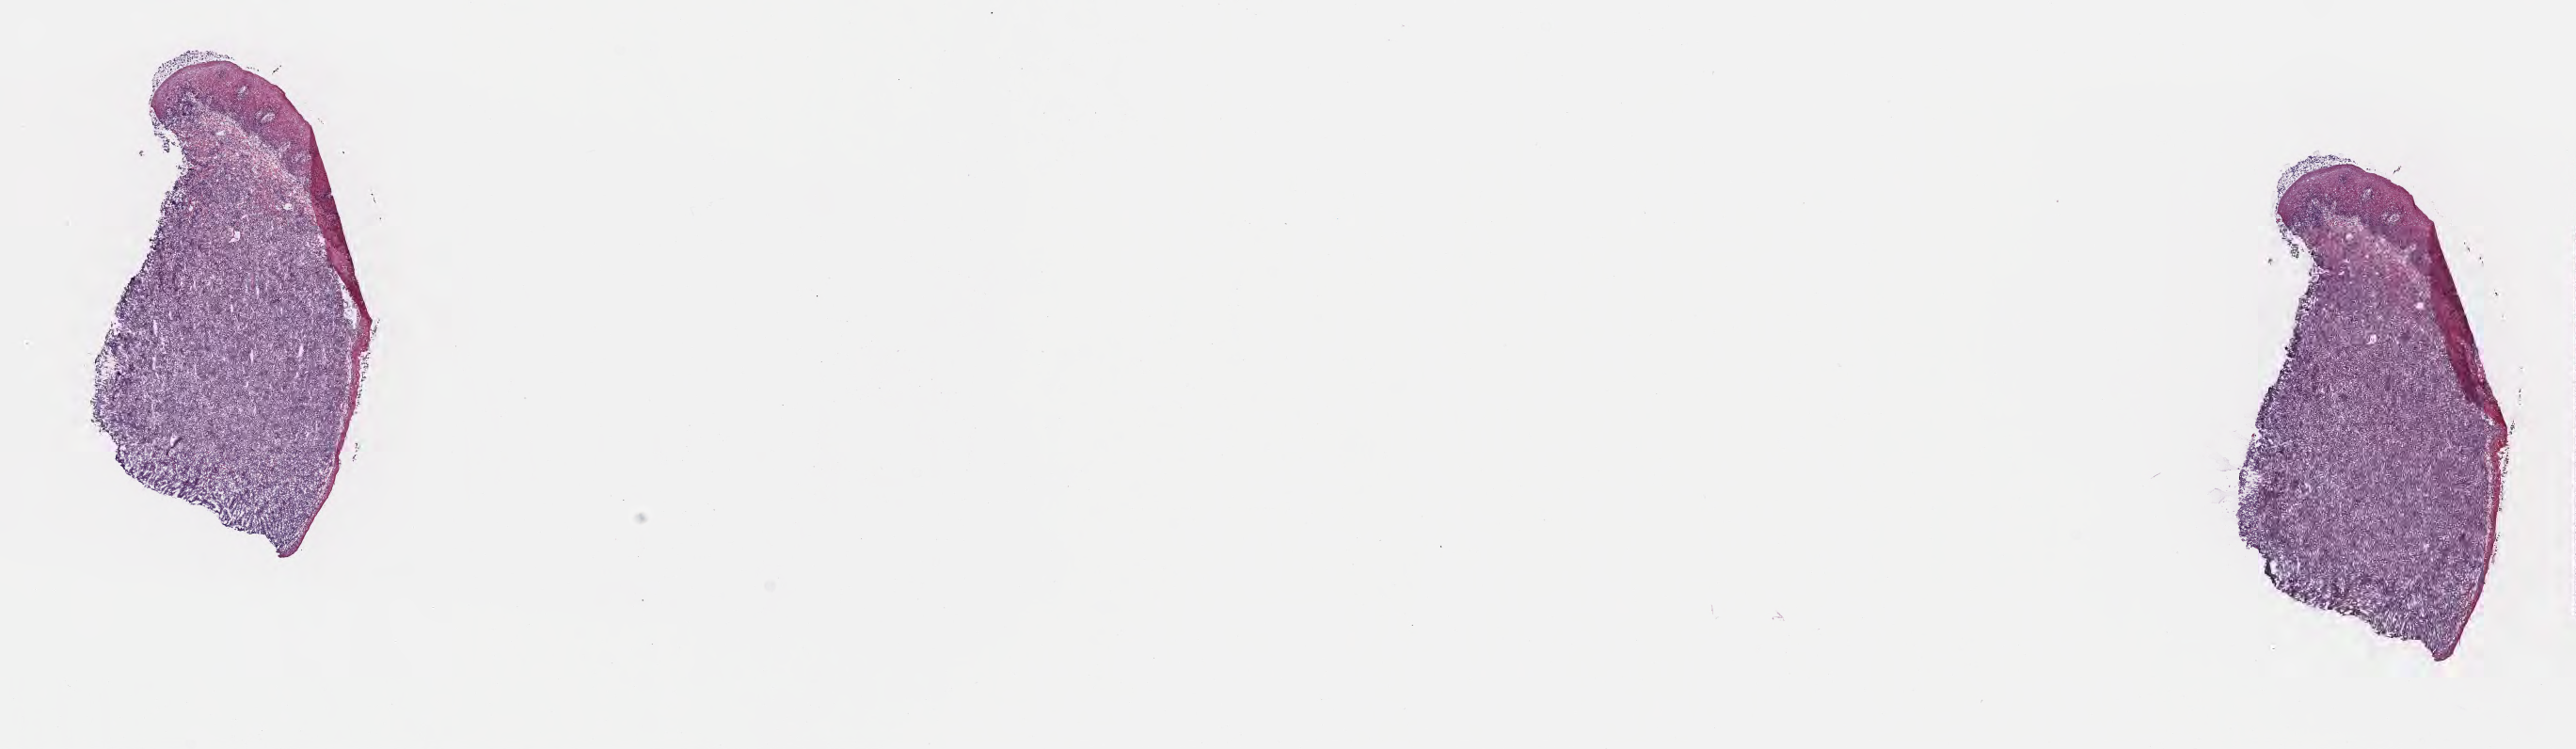
H&E whole-slide image — whole scanned area (about 22.1 x 6.4 mm) shown as a low-resolution overview, frozen section, primary tumor, anatomic site: cranium. Male patient, 10 years old. Composition of this section per pathologist review: tumor cells 80%, tumor nuclei 90%, stromal cells 10%, necrosis 10%, normal cells 0%. Infiltration values recorded for this section: lymphocyte infiltration 15%, monocyte infiltration 60%, neutrophil infiltration 10%.
Ann Arbor stage (patient): Stage I. Section: bottom of the tissue portion. Histologic diagnosis: Burkitt lymphoma, NOS.